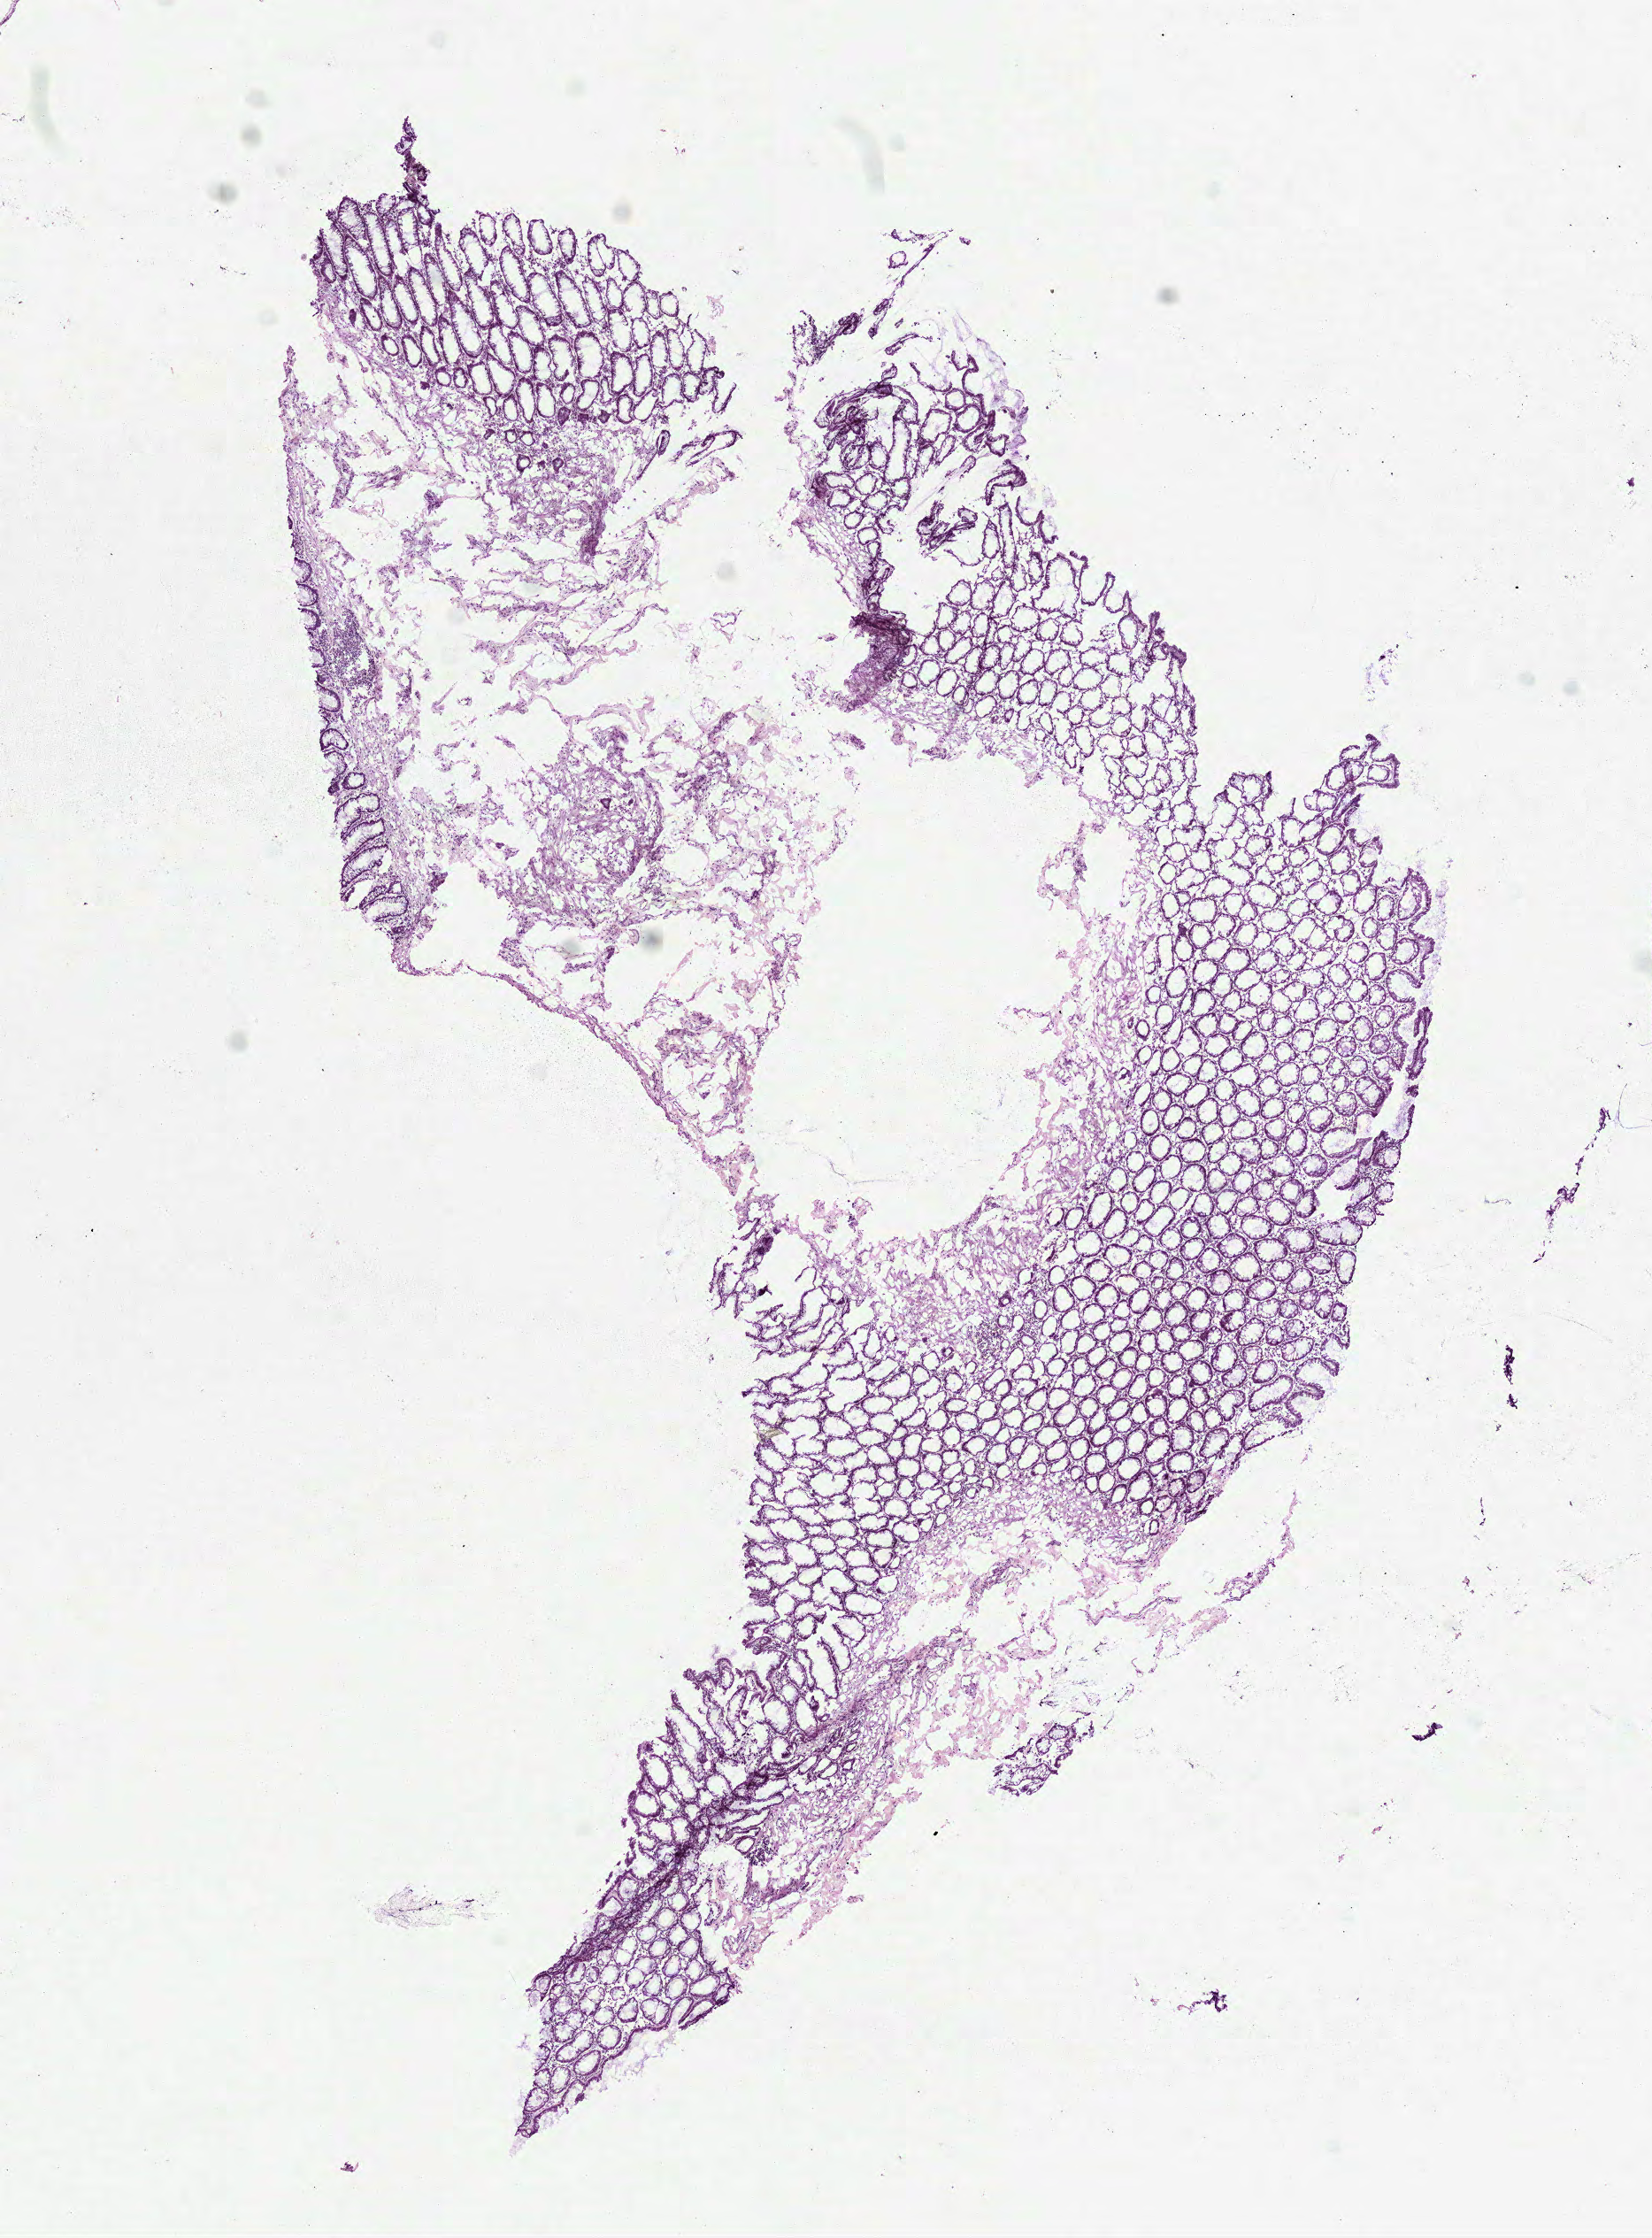
Whole-slide histology image, Hematoxylin and eosin (H&E) stained, whole scanned area (about 7.5 x 10.2 mm, from a 40x scan) shown as a low-resolution overview. Frozen section from the top of the tissue portion. Sample: solid tissue normal (non-tumour tissue), colon. Male, age 65 years at initial diagnosis.
This section: solid tissue normal sample (biorepository sample class). Patient diagnosis: Mucinous adenocarcinoma (descending colon).